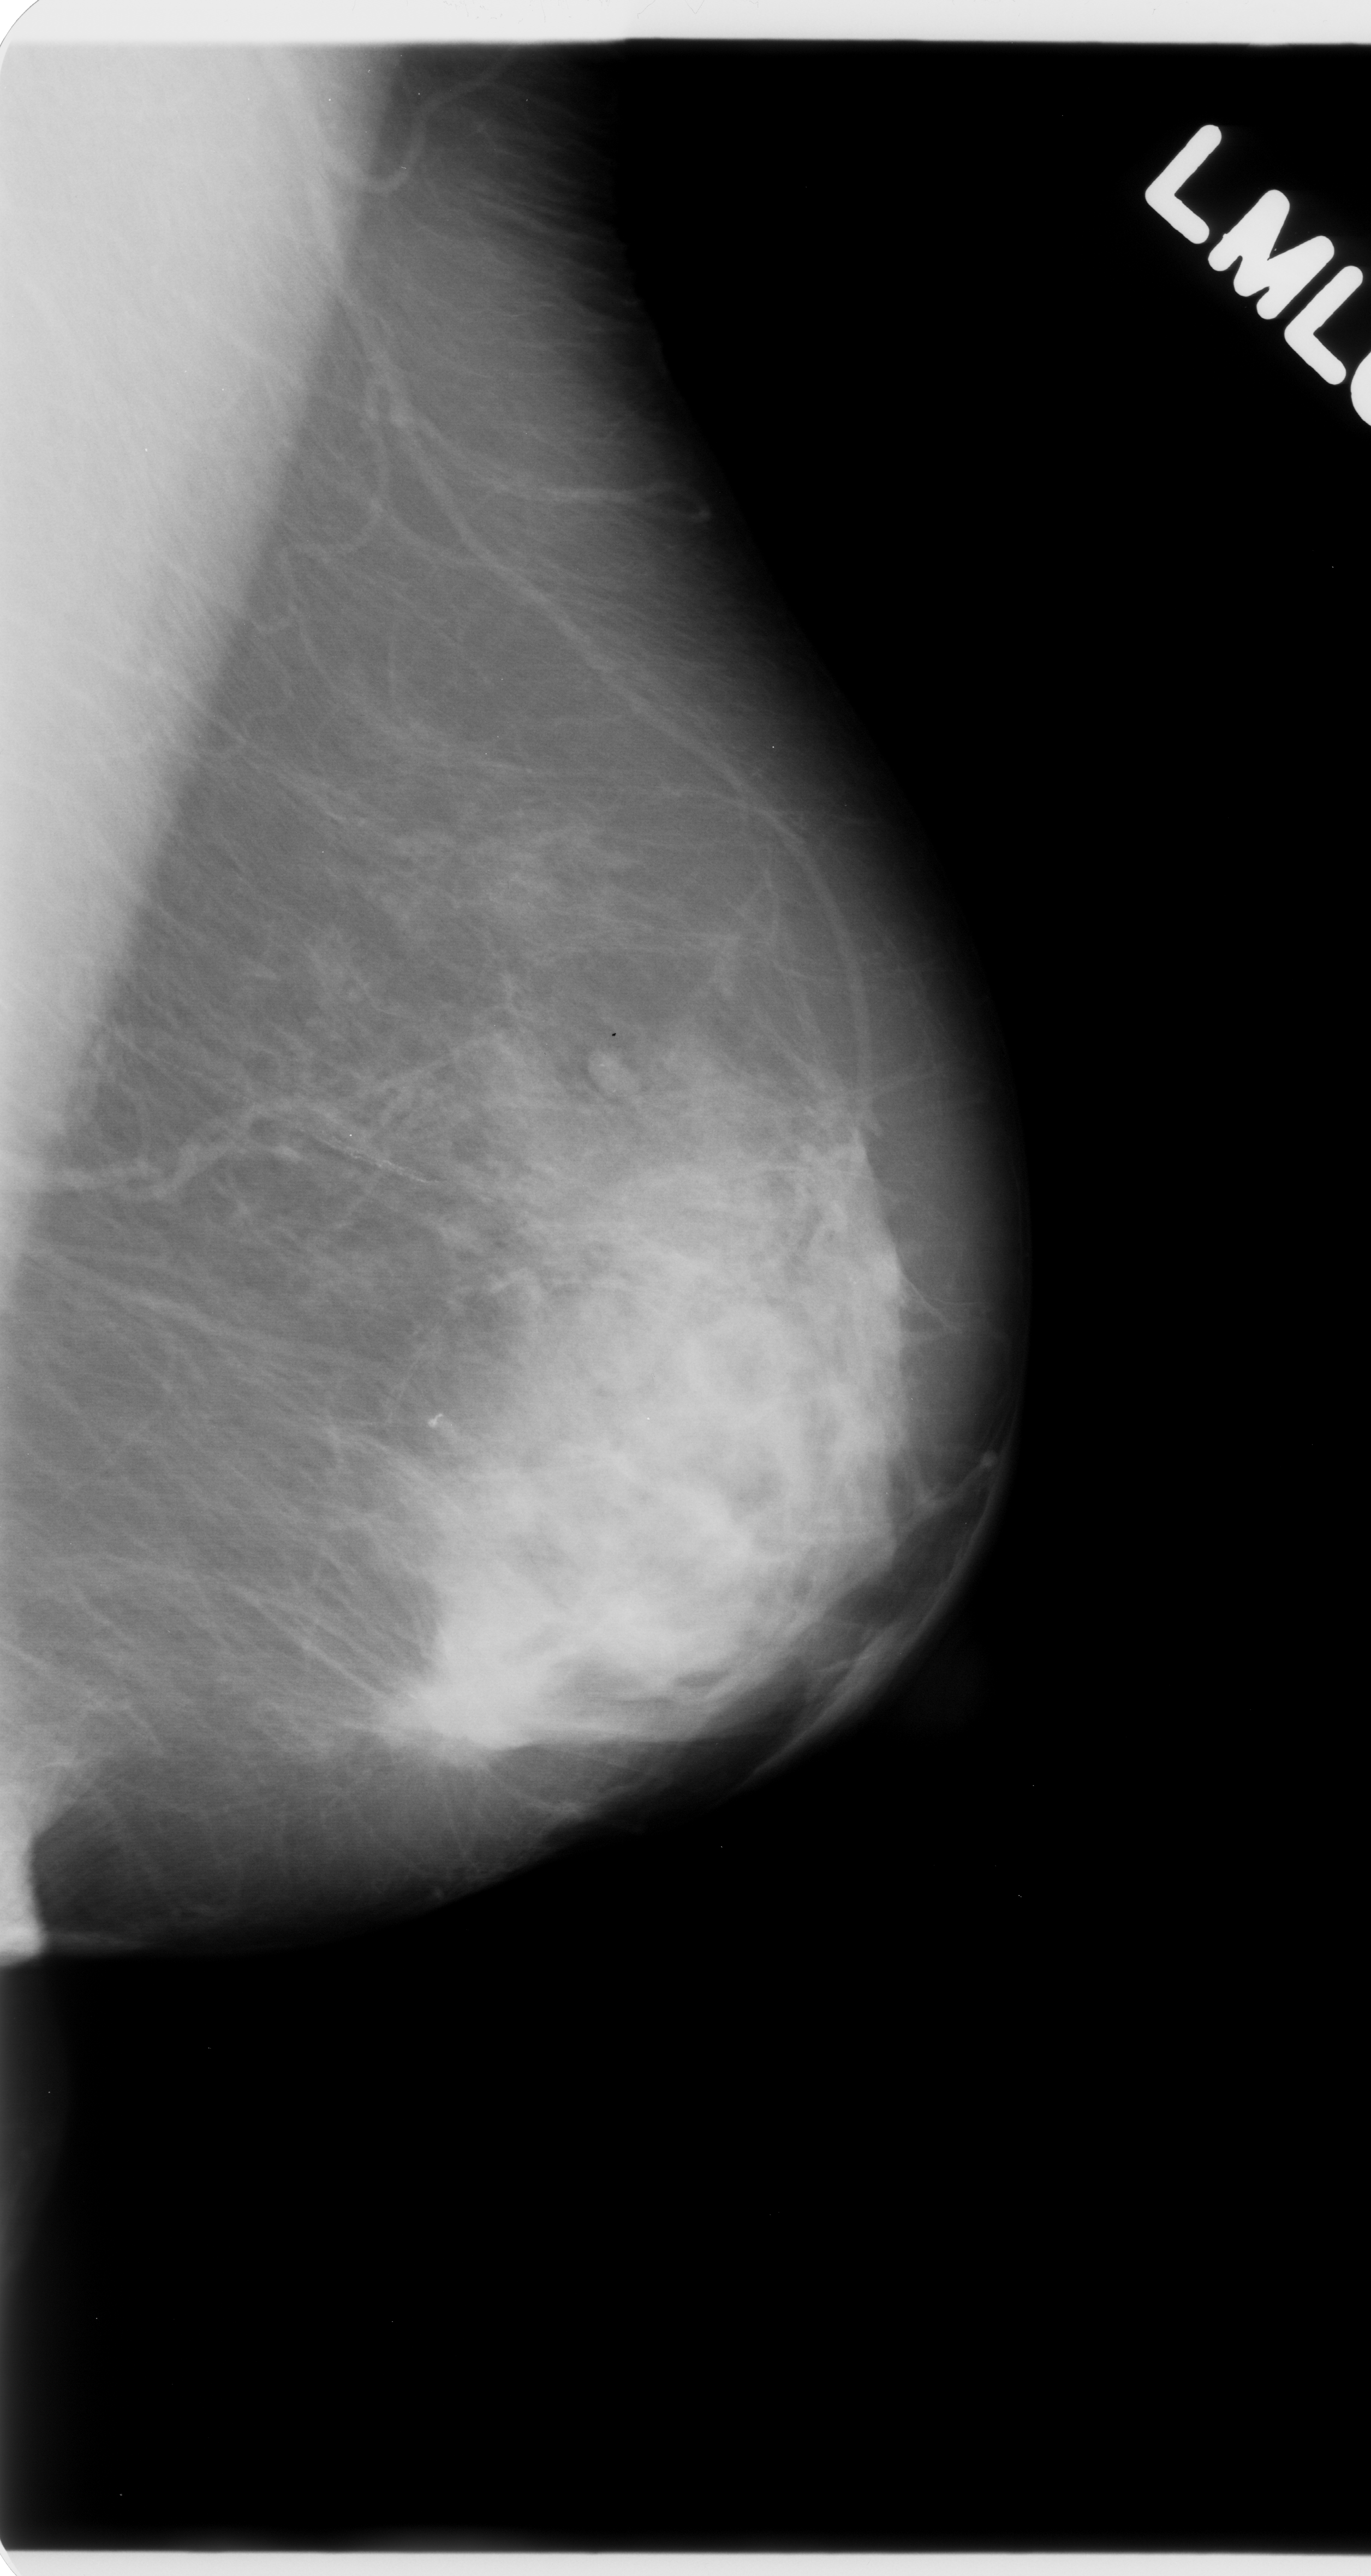
Digitized screen-film mammogram; left breast; MLO view; BI-RADS breast density category 3 (scale 1–4); 1371 × 2576 image matrix.
Expert-marked regions of interest on this film, with their recorded descriptors:
- mass, shape lobulated, margins spiculated; BI-RADS assessment category 5; subtlety rating 5 on a 1 (subtle) to 5 (obvious) scale; pathology (as recorded): malignant: bounding box (x1, y1, x2, y2) in pixels: (394, 1601, 556, 1753)